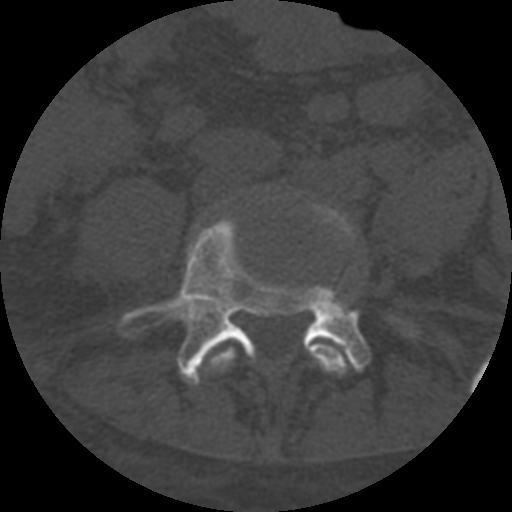
CT including the spine, one axial slice; slice 193 of 708 in the series (ordered by position); reconstruction kernel STANDARD; one of 3 acquisitions stored at this slice position; bone window (W 1800 / L 400 HU); 1.25 mm slice thickness; 512 × 512 image matrix. Patient age 55 years. Case-level facts recorded for this patient, not image findings: primary cancer: colon; vertebrae with lytic lesions (as recorded): T12, L1, L5.
Annotated regions visible in this slice (semi-automatically segmented with operator editing):
- L4 vertebra: box from (x=205, y=204) to (x=356, y=375) px
- L5 vertebra: (x=117, y=217)–(x=423, y=385)